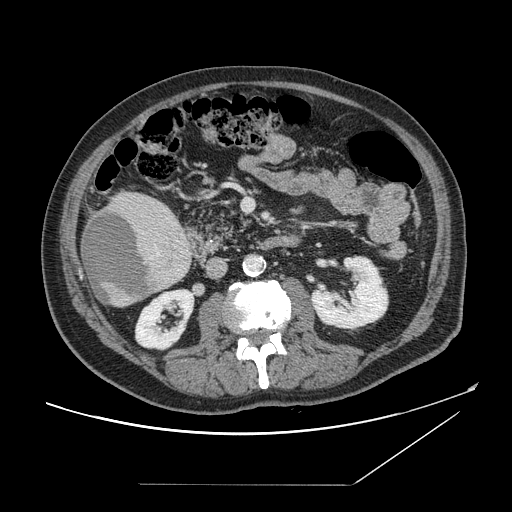
Contrast-enhanced abdominal CT, one axial slice; slice 55 of 166 in the series (ordered by position); intravenous contrast given; soft-tissue window (W 400 / L 40 HU); 2.5 mm slice thickness; 512 × 512 image matrix. Male patient, age 80 years. Case-level facts recorded for this patient, not image findings: diagnosis: colorectal cancer liver metastases, imaged before liver resection; multiple liver metastases: no; largest metastasis: 2.2 cm; disease in both lobes: no.
Structures marked on this image (manually delineated by an expert):
- liver: box from (x=81, y=192) to (x=192, y=307) px
- liver metastasis: (x=82, y=209)–(x=154, y=303)